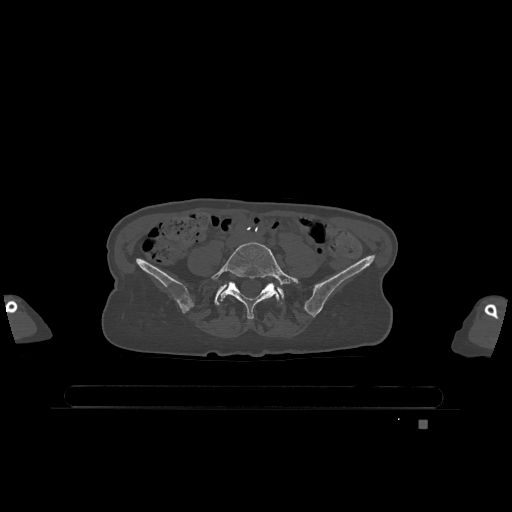
CT including the spine, one axial slice; position 239 of 1317 along the scan axis; bone window (W 1800 / L 400 HU); 0.5 mm slice thickness; 512 × 512 image matrix. Patient: female, 74 years. From the clinical record (not read from this slice): primary cancer: lung; vertebrae with lytic lesions (as recorded): T1, T4, T5, T6, L4, L5.
Structures marked on this image (semi-automatically segmented with operator editing):
- L5 vertebra: bounding box (x1, y1, x2, y2) in pixels: (211, 242, 299, 319)